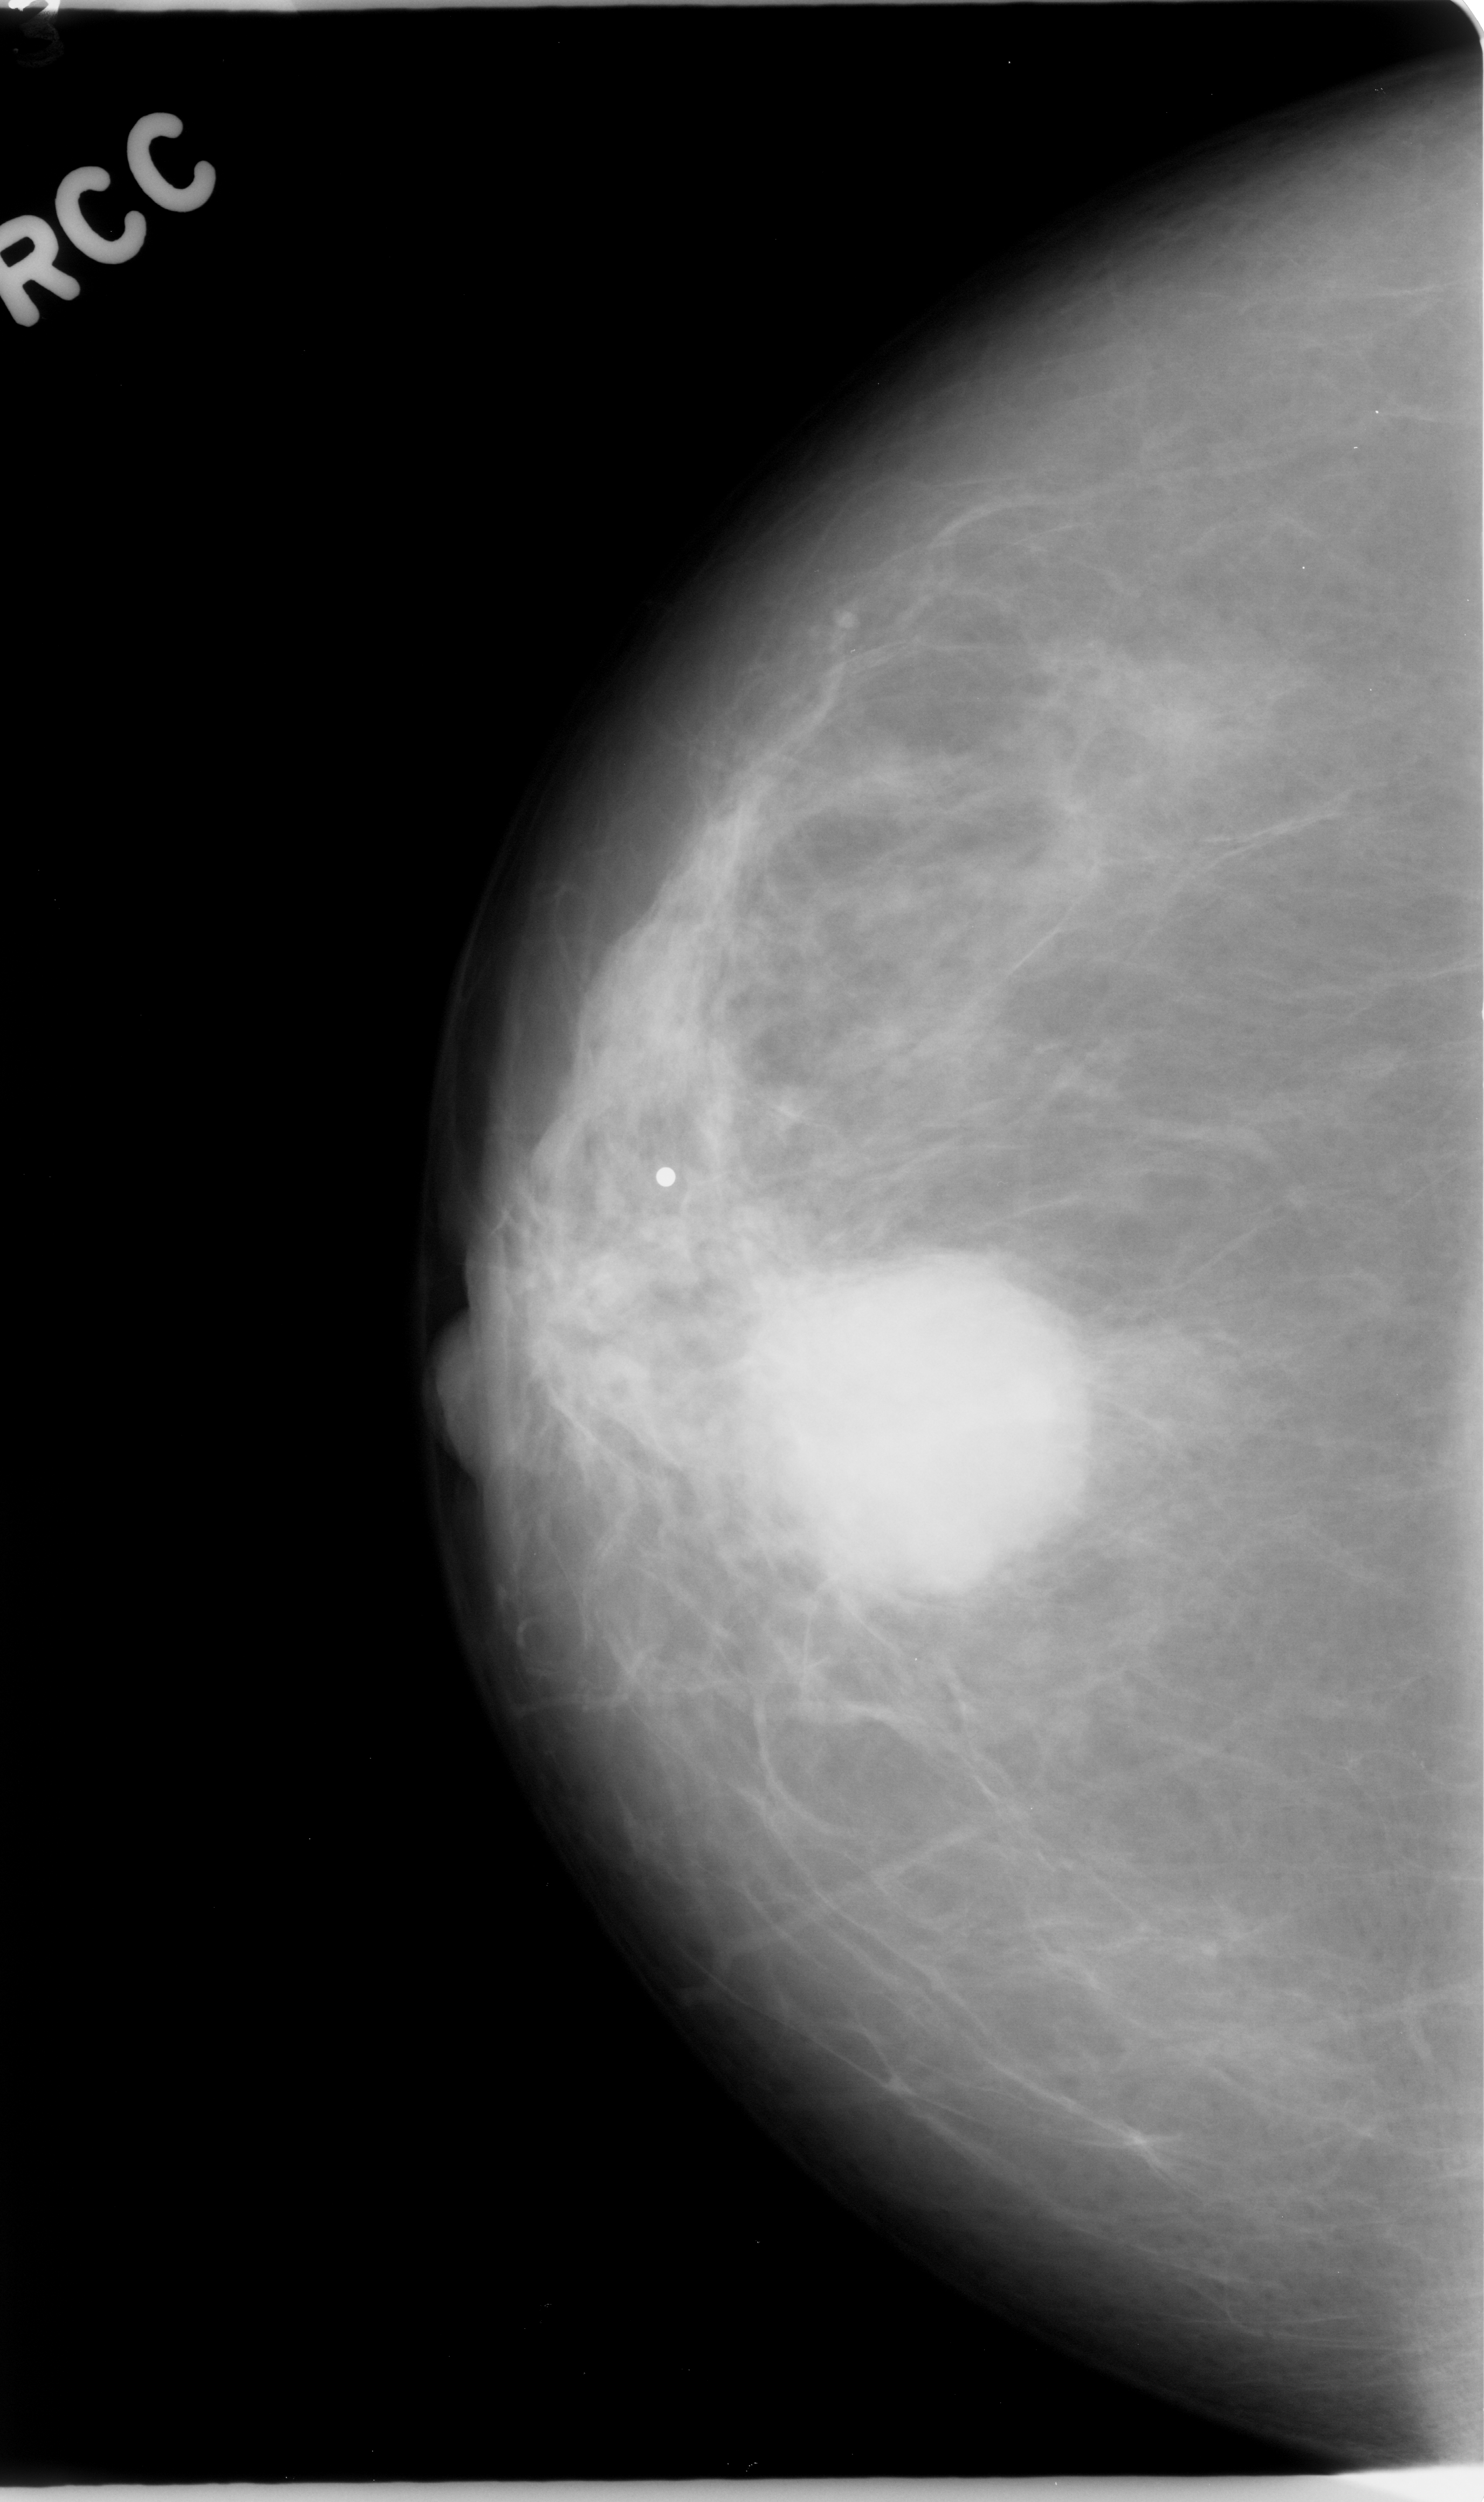
Mammogram (digitized film), right breast, CC view, BI-RADS breast density category 1 (scale 1–4).
Finding: mass, shape lobulated, margins microlobulated; BI-RADS assessment category 5; pathology result (as recorded, not read from the image): malignant.